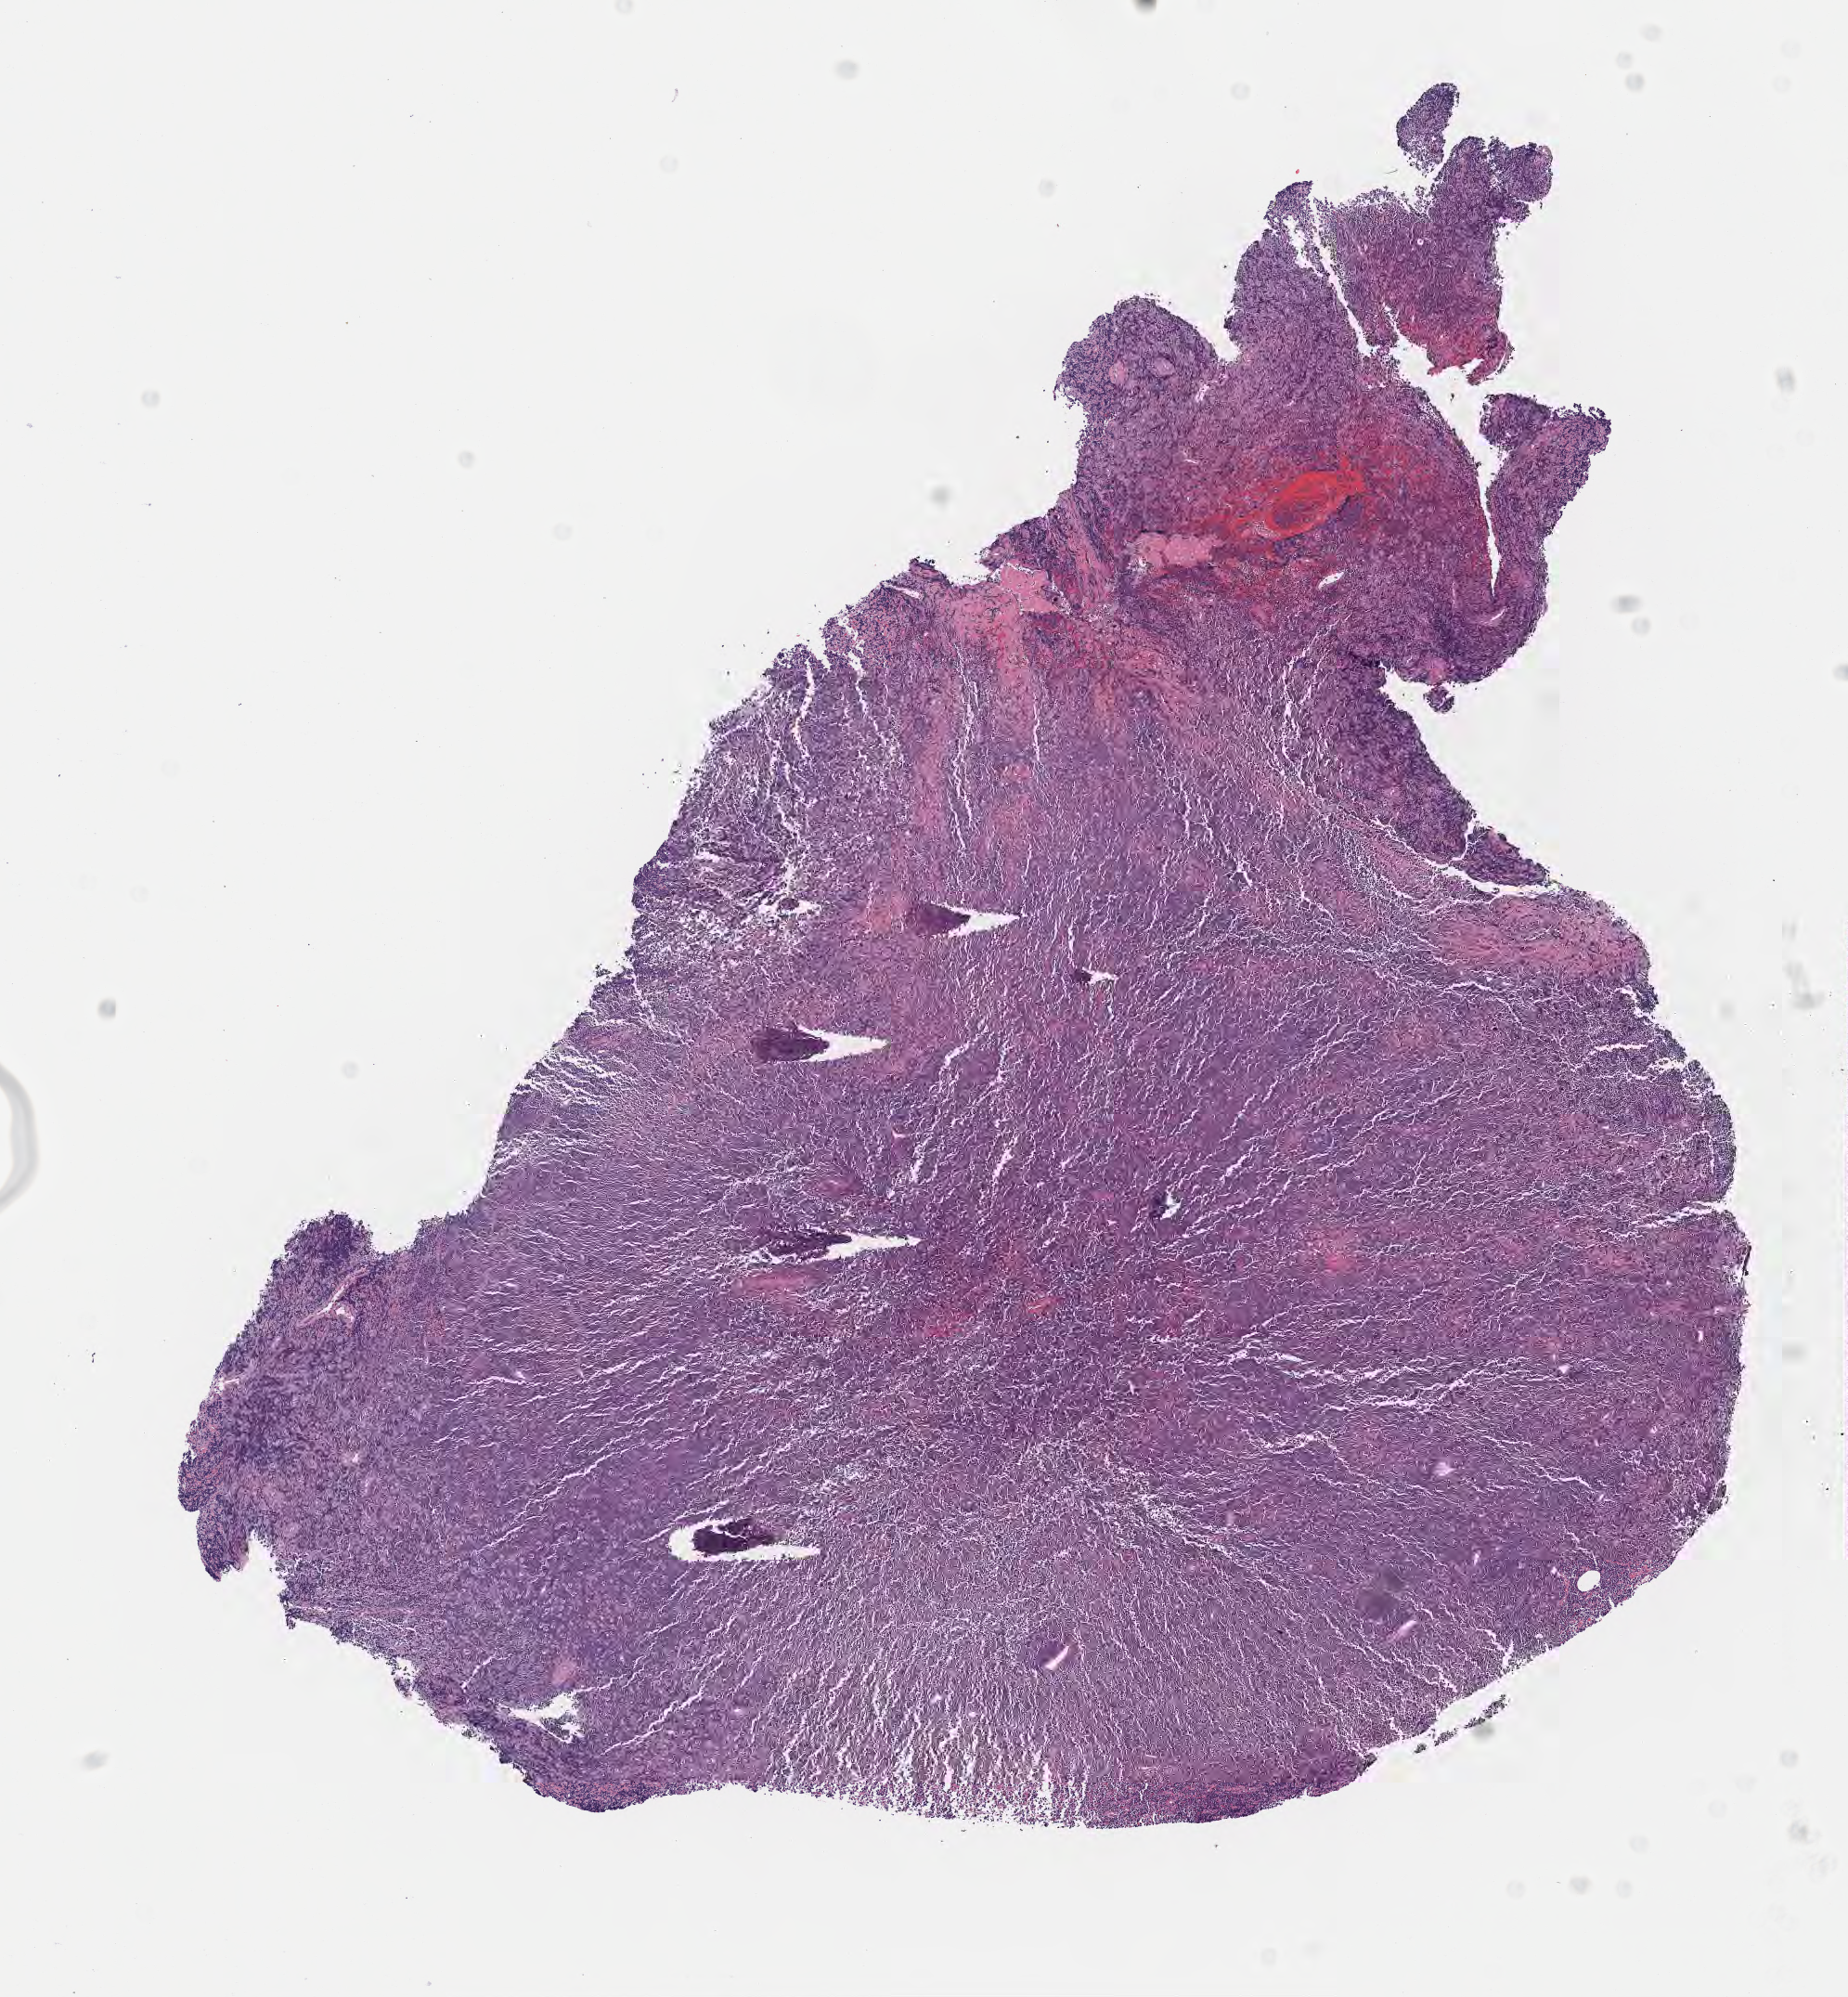
Whole-slide image, haematoxylin and eosin stain — a low-resolution overview of the entire scanned area, about 8.1 x 8.7 mm. Specimen: tumor tissue. Anatomic site: mandible. Female, age 5 years at initial diagnosis.
- histologic diagnosis: Burkitt lymphoma, NOS